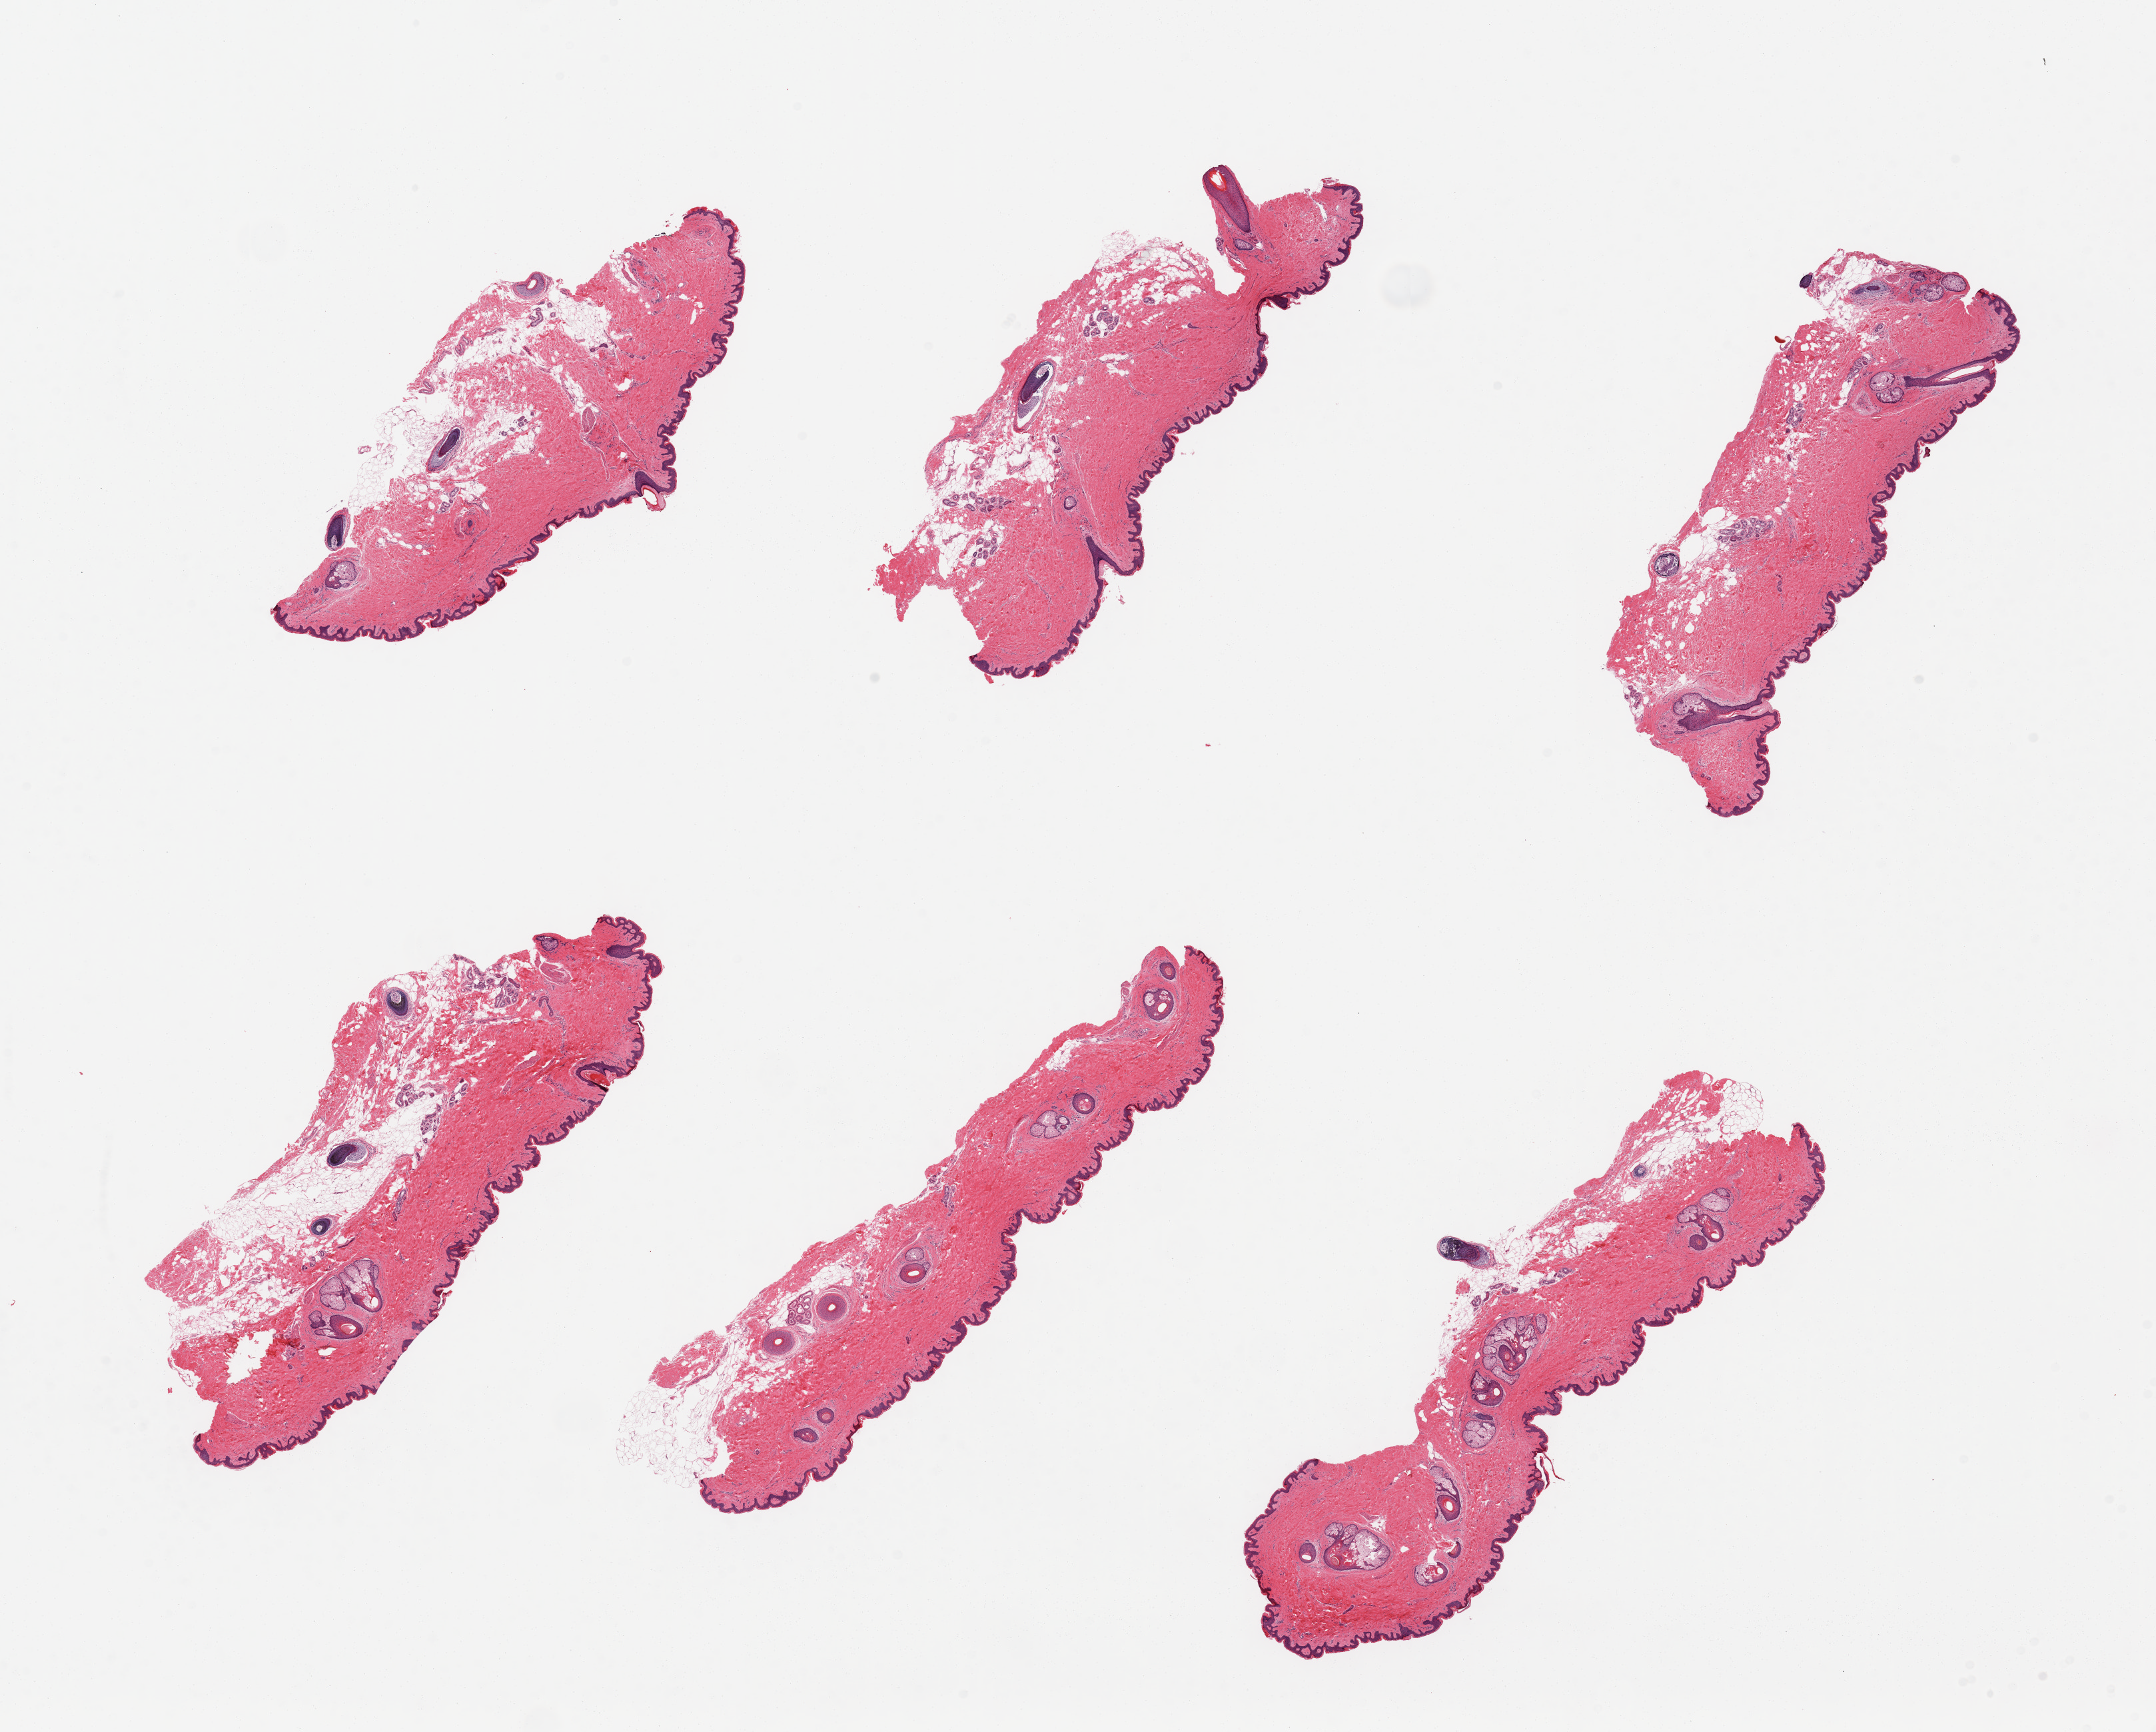
Hematoxylin and eosin (H&E) whole-slide image, a low-resolution overview of the entire scanned area, about 25.6 x 20.6 mm. PAXgene-fixed, paraffin-embedded tissue. Target tissue: skin of suprapubic region. Tissue donor sample. Donor: male.
Review note (as recorded): 6 pieces, minimal dermal fat; squamous epithelium is ~50-80 microns.